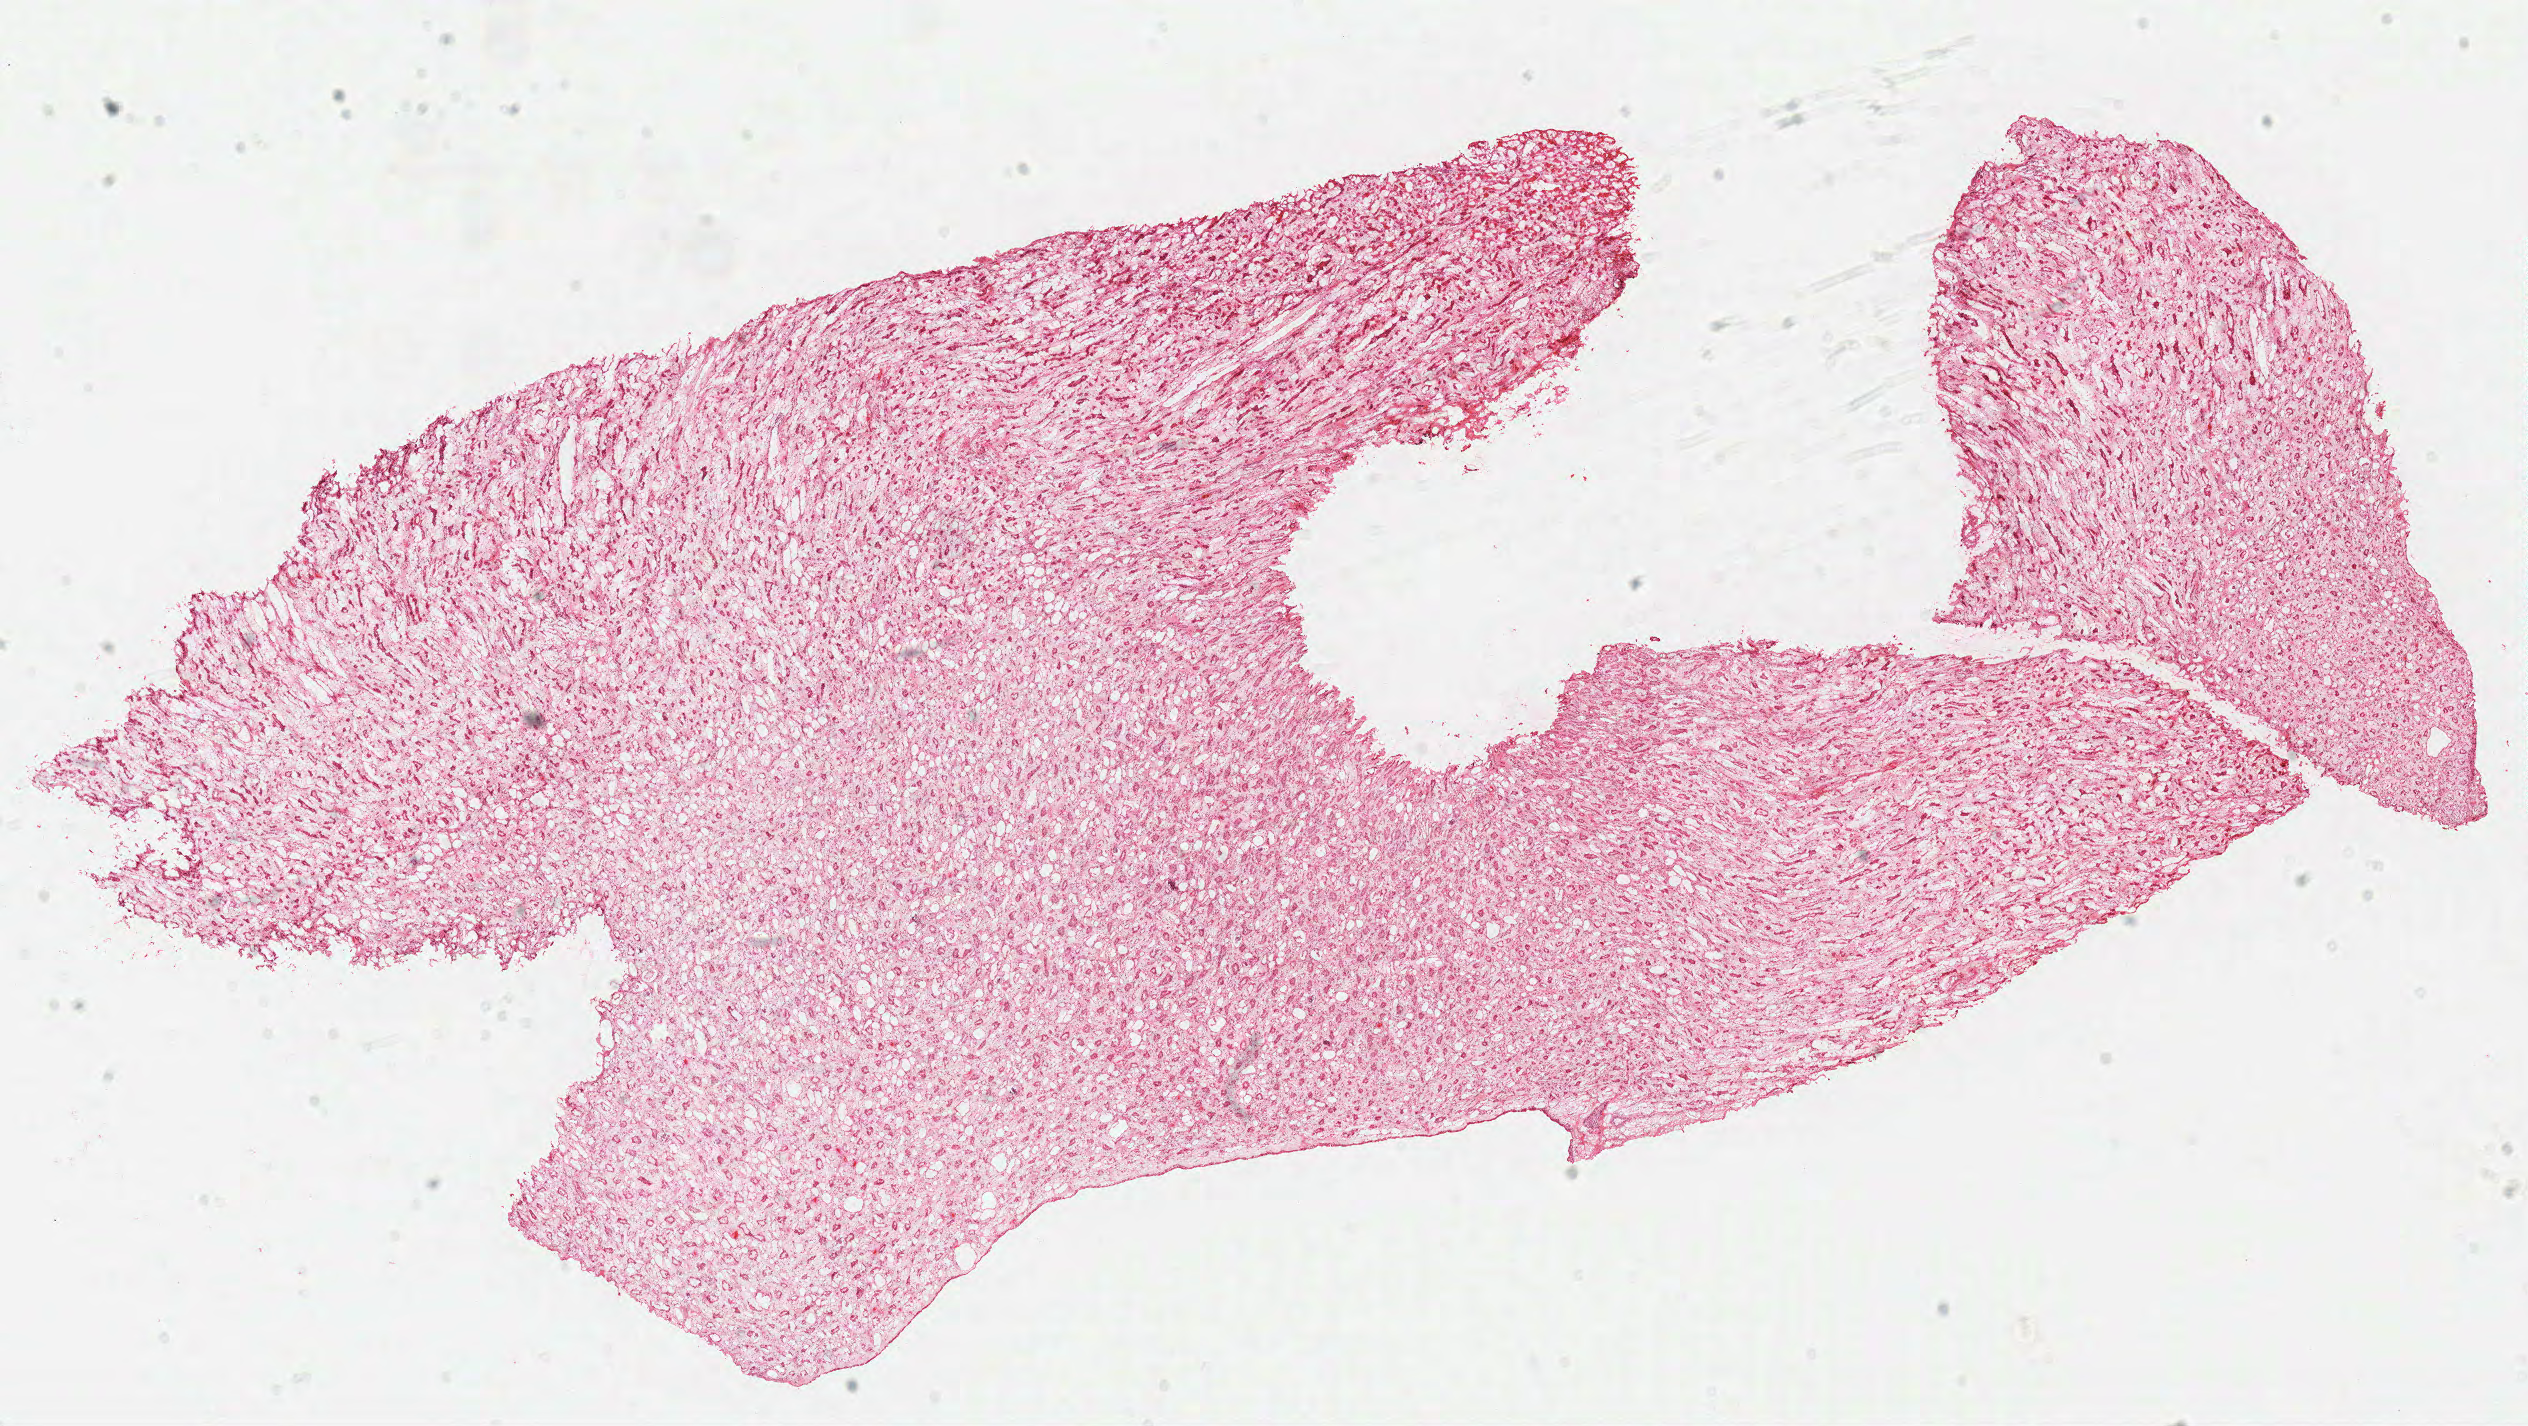
Whole-slide histology image, H&E-stained — a low-resolution overview of the entire scanned area, about 19.9 x 11.2 mm (from a 40x scan), frozen section from the top of the tissue portion, solid tissue normal (non-tumour tissue) sample from the kidney. Male, age 60 years at initial diagnosis.
- this section: solid tissue normal (non-tumour) sample from the same patient
- patient diagnosis: Clear cell adenocarcinoma, NOS